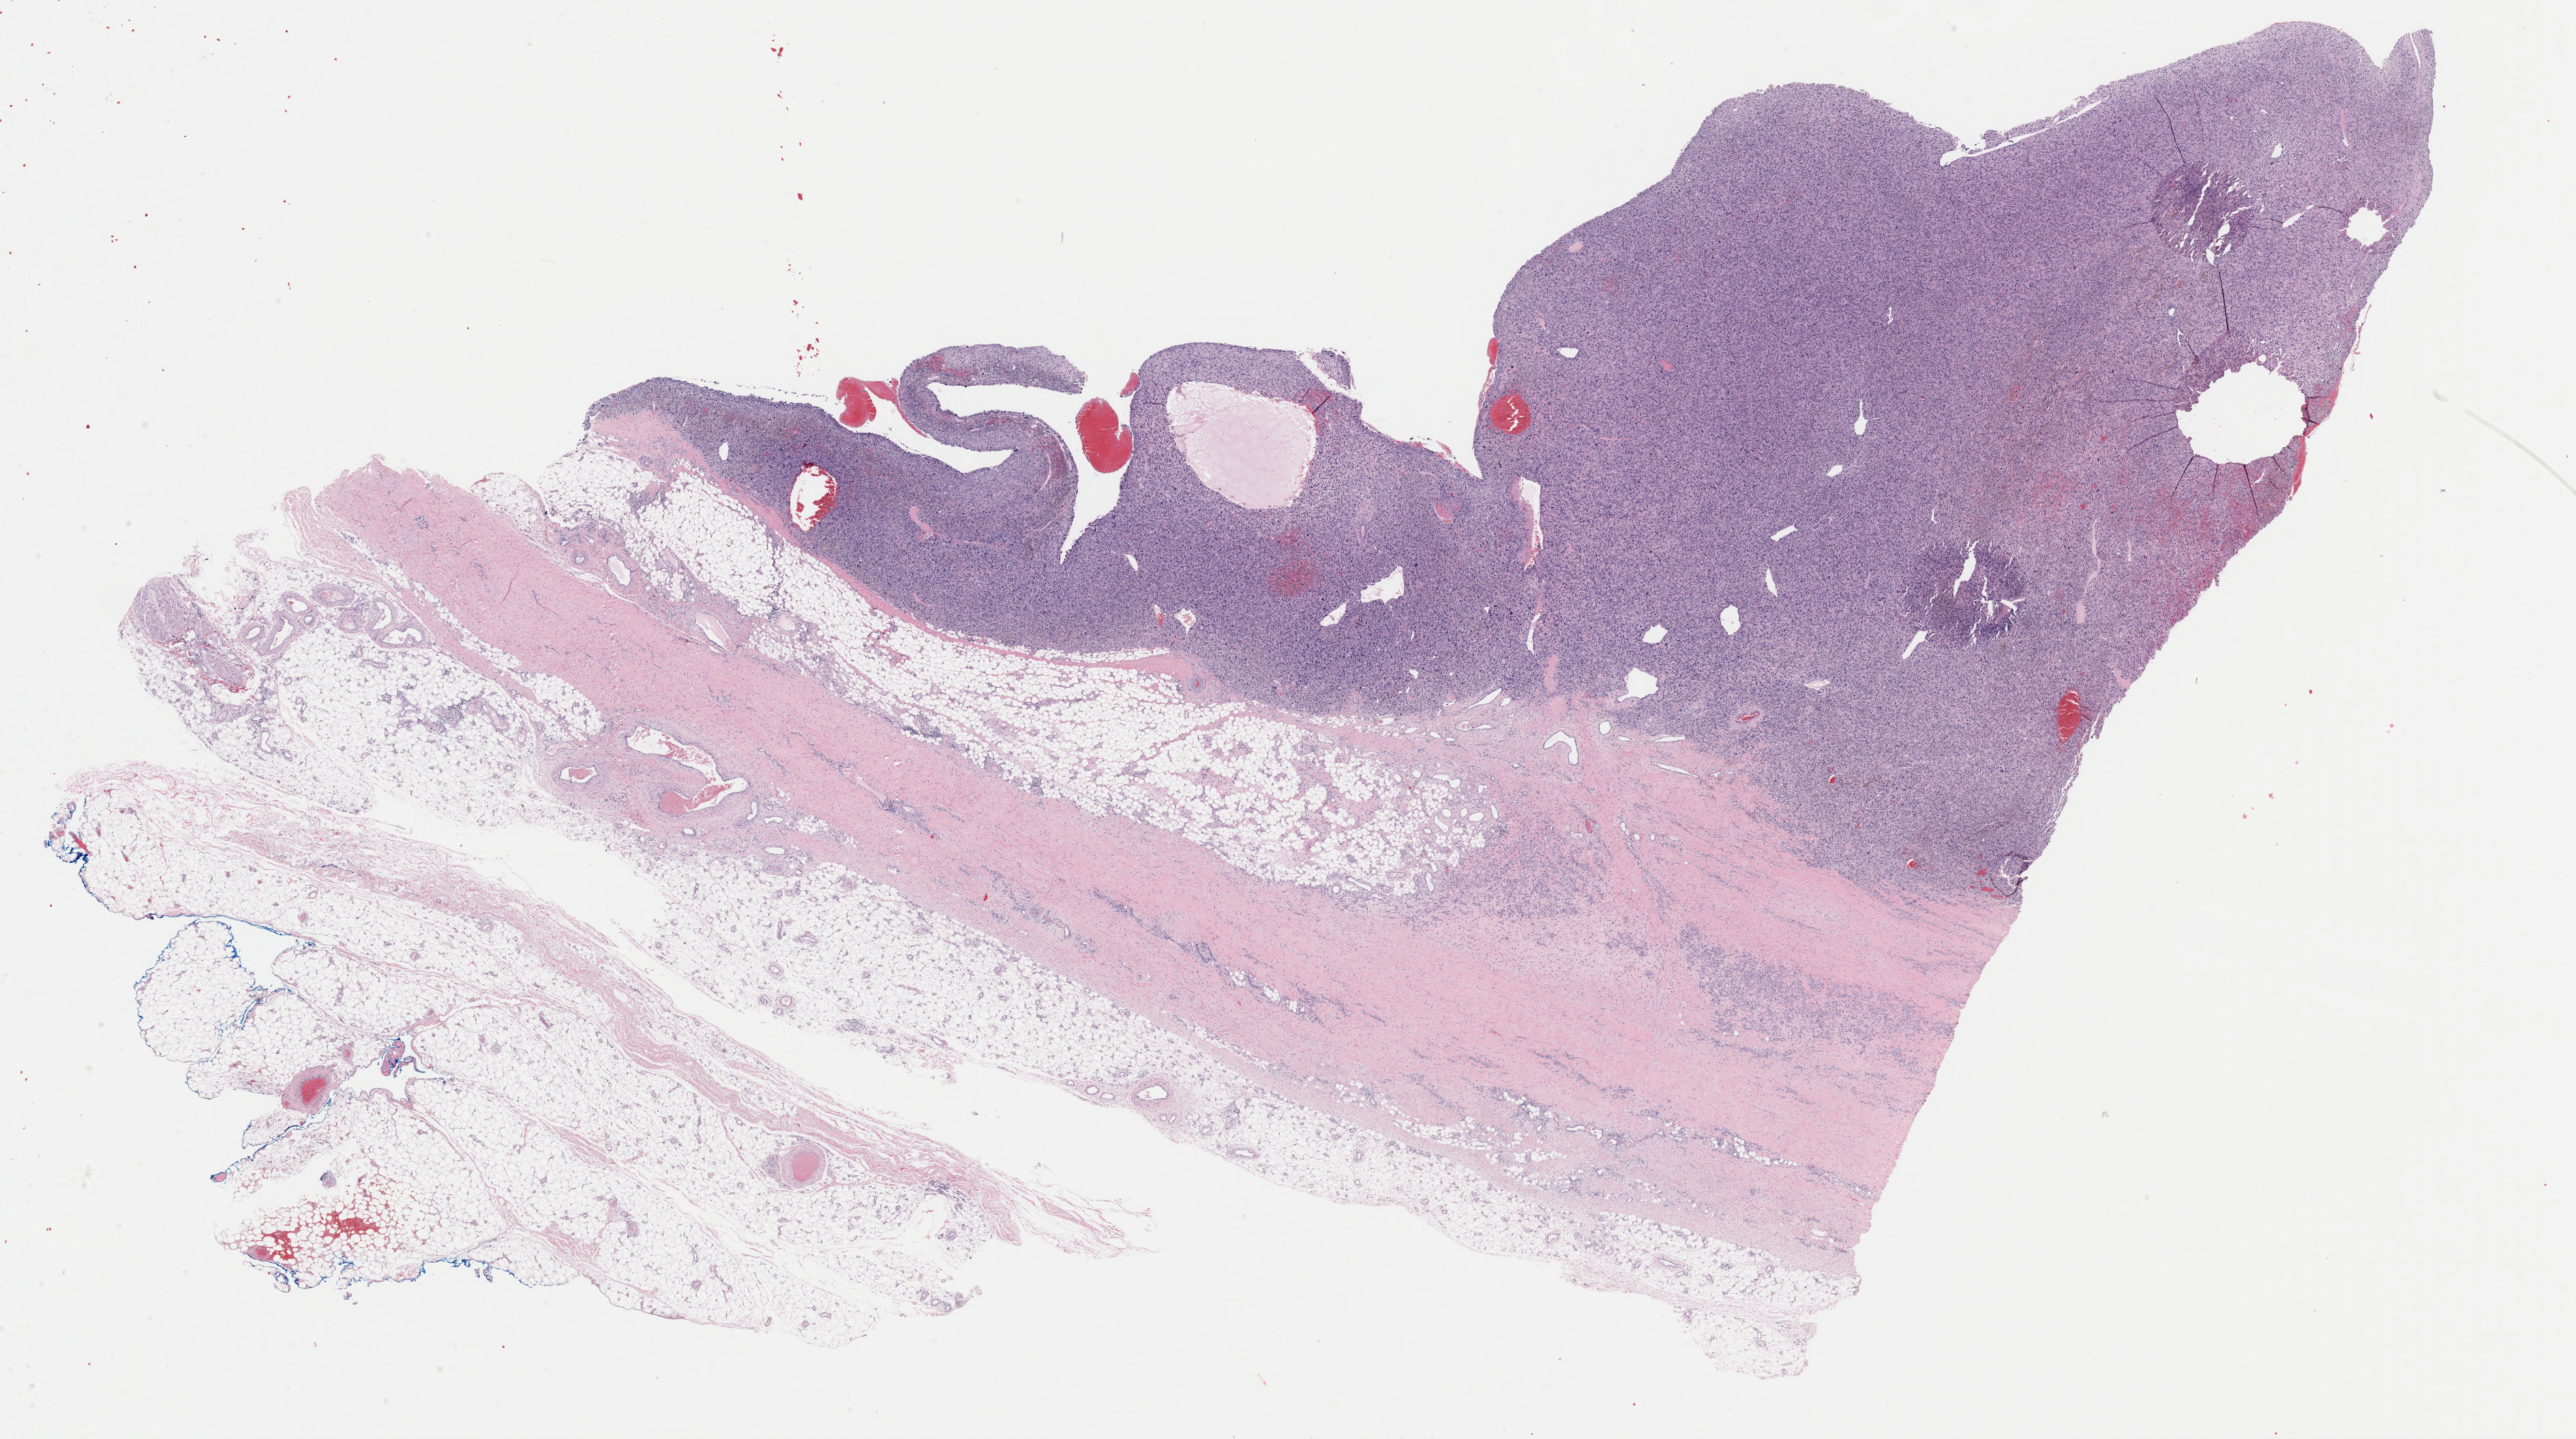
Whole-slide histology image, Hematoxylin and eosin (H&E) stained, a low-resolution overview of the entire scanned area, about 29.8 x 16.7 mm; formalin-fixed paraffin-embedded (FFPE) diagnostic section; connective, subcutaneous and other soft tissues, primary tumour sample. Female patient; age at initial diagnosis 75 years.
- diagnosis: Malignant fibrous histiocytoma (connective, subcutaneous and other soft tissues of lower limb and hip)